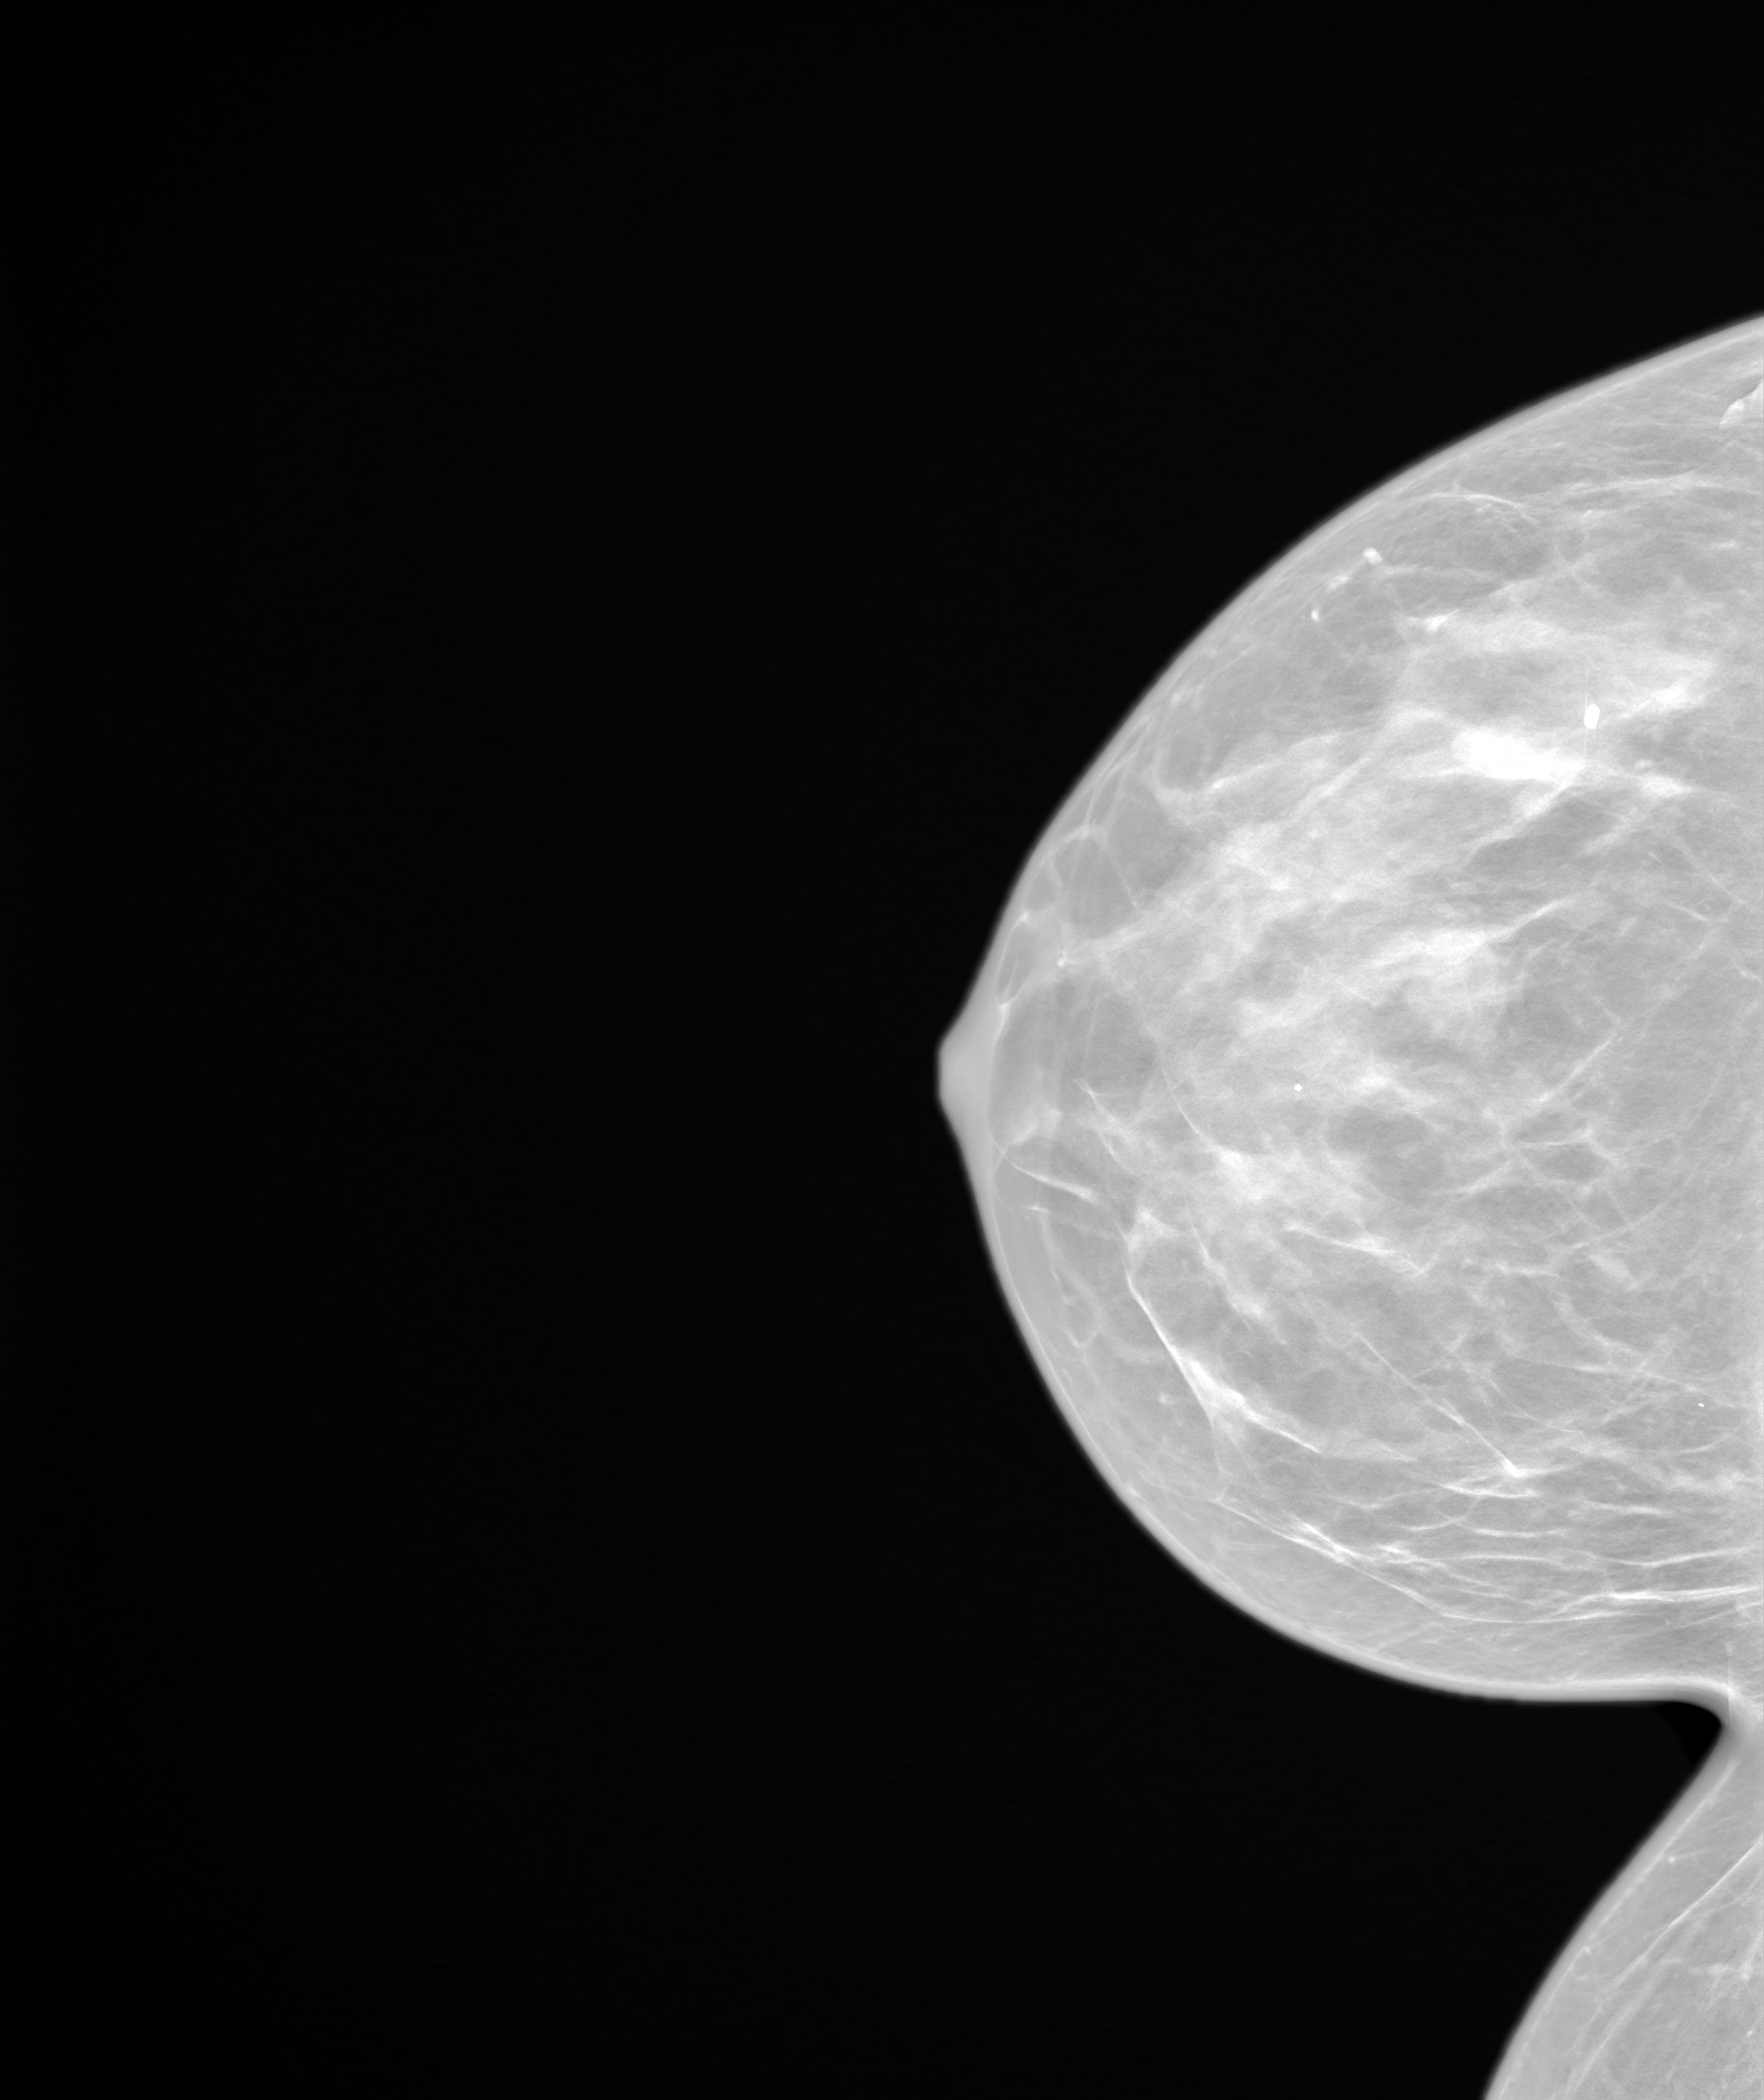
Screening examination. Patient: female, 52 years.
Image type: synthesized 2-D view from tomosynthesis. Breast: right. Projection: CC view.